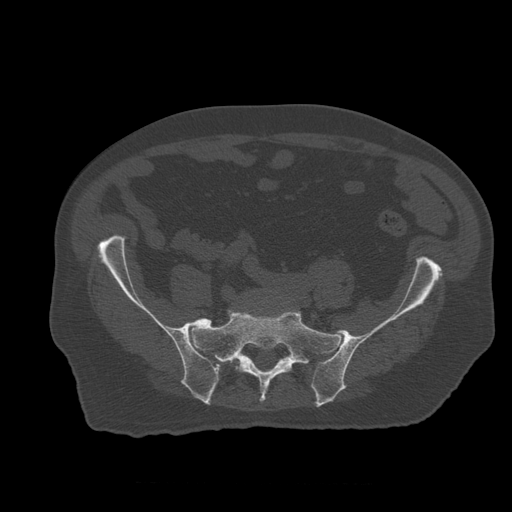
CT including the spine, one axial slice. Position 122 of 399 along the scan axis. Reconstruction kernel STANDARD. 120 kVp. Bone window (W 1800 / L 400 HU). 512 × 512 image matrix. Patient age 73 years. From the clinical record (not read from this slice): primary cancer: prostate; vertebrae with lytic lesions (as recorded): L2.
Structures marked on this image (semi-automatically segmented with operator editing):
- L5 vertebra: bounding box <215,360,232,380> (left, top, right, bottom; pixels)